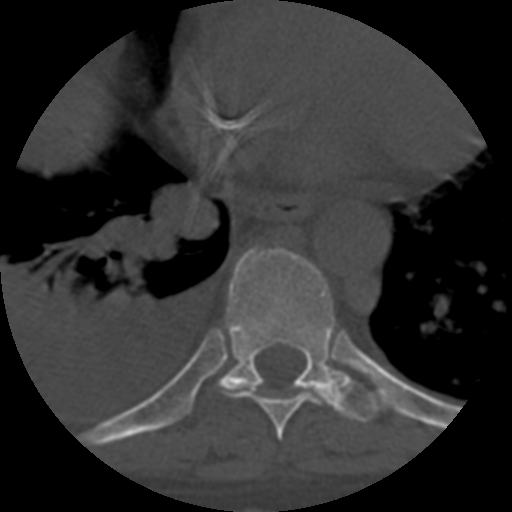
CT including the spine, one axial slice. Slice 385 of 708 in the series (ordered by position). 120 kVp. One of 3 acquisitions stored at this slice position. Bone window (W 1800 / L 400 HU). 512 × 512 image matrix, field of view 160 × 160 mm. Patient age 55 years. Case-level facts recorded for this patient, not image findings: primary cancer: colon.
Annotated regions visible in this slice (semi-automatically segmented with operator editing):
- T8 vertebra: bounding box (x1, y1, x2, y2) in pixels: (257, 392, 323, 440)
- T9 vertebra: (217, 247, 377, 423)